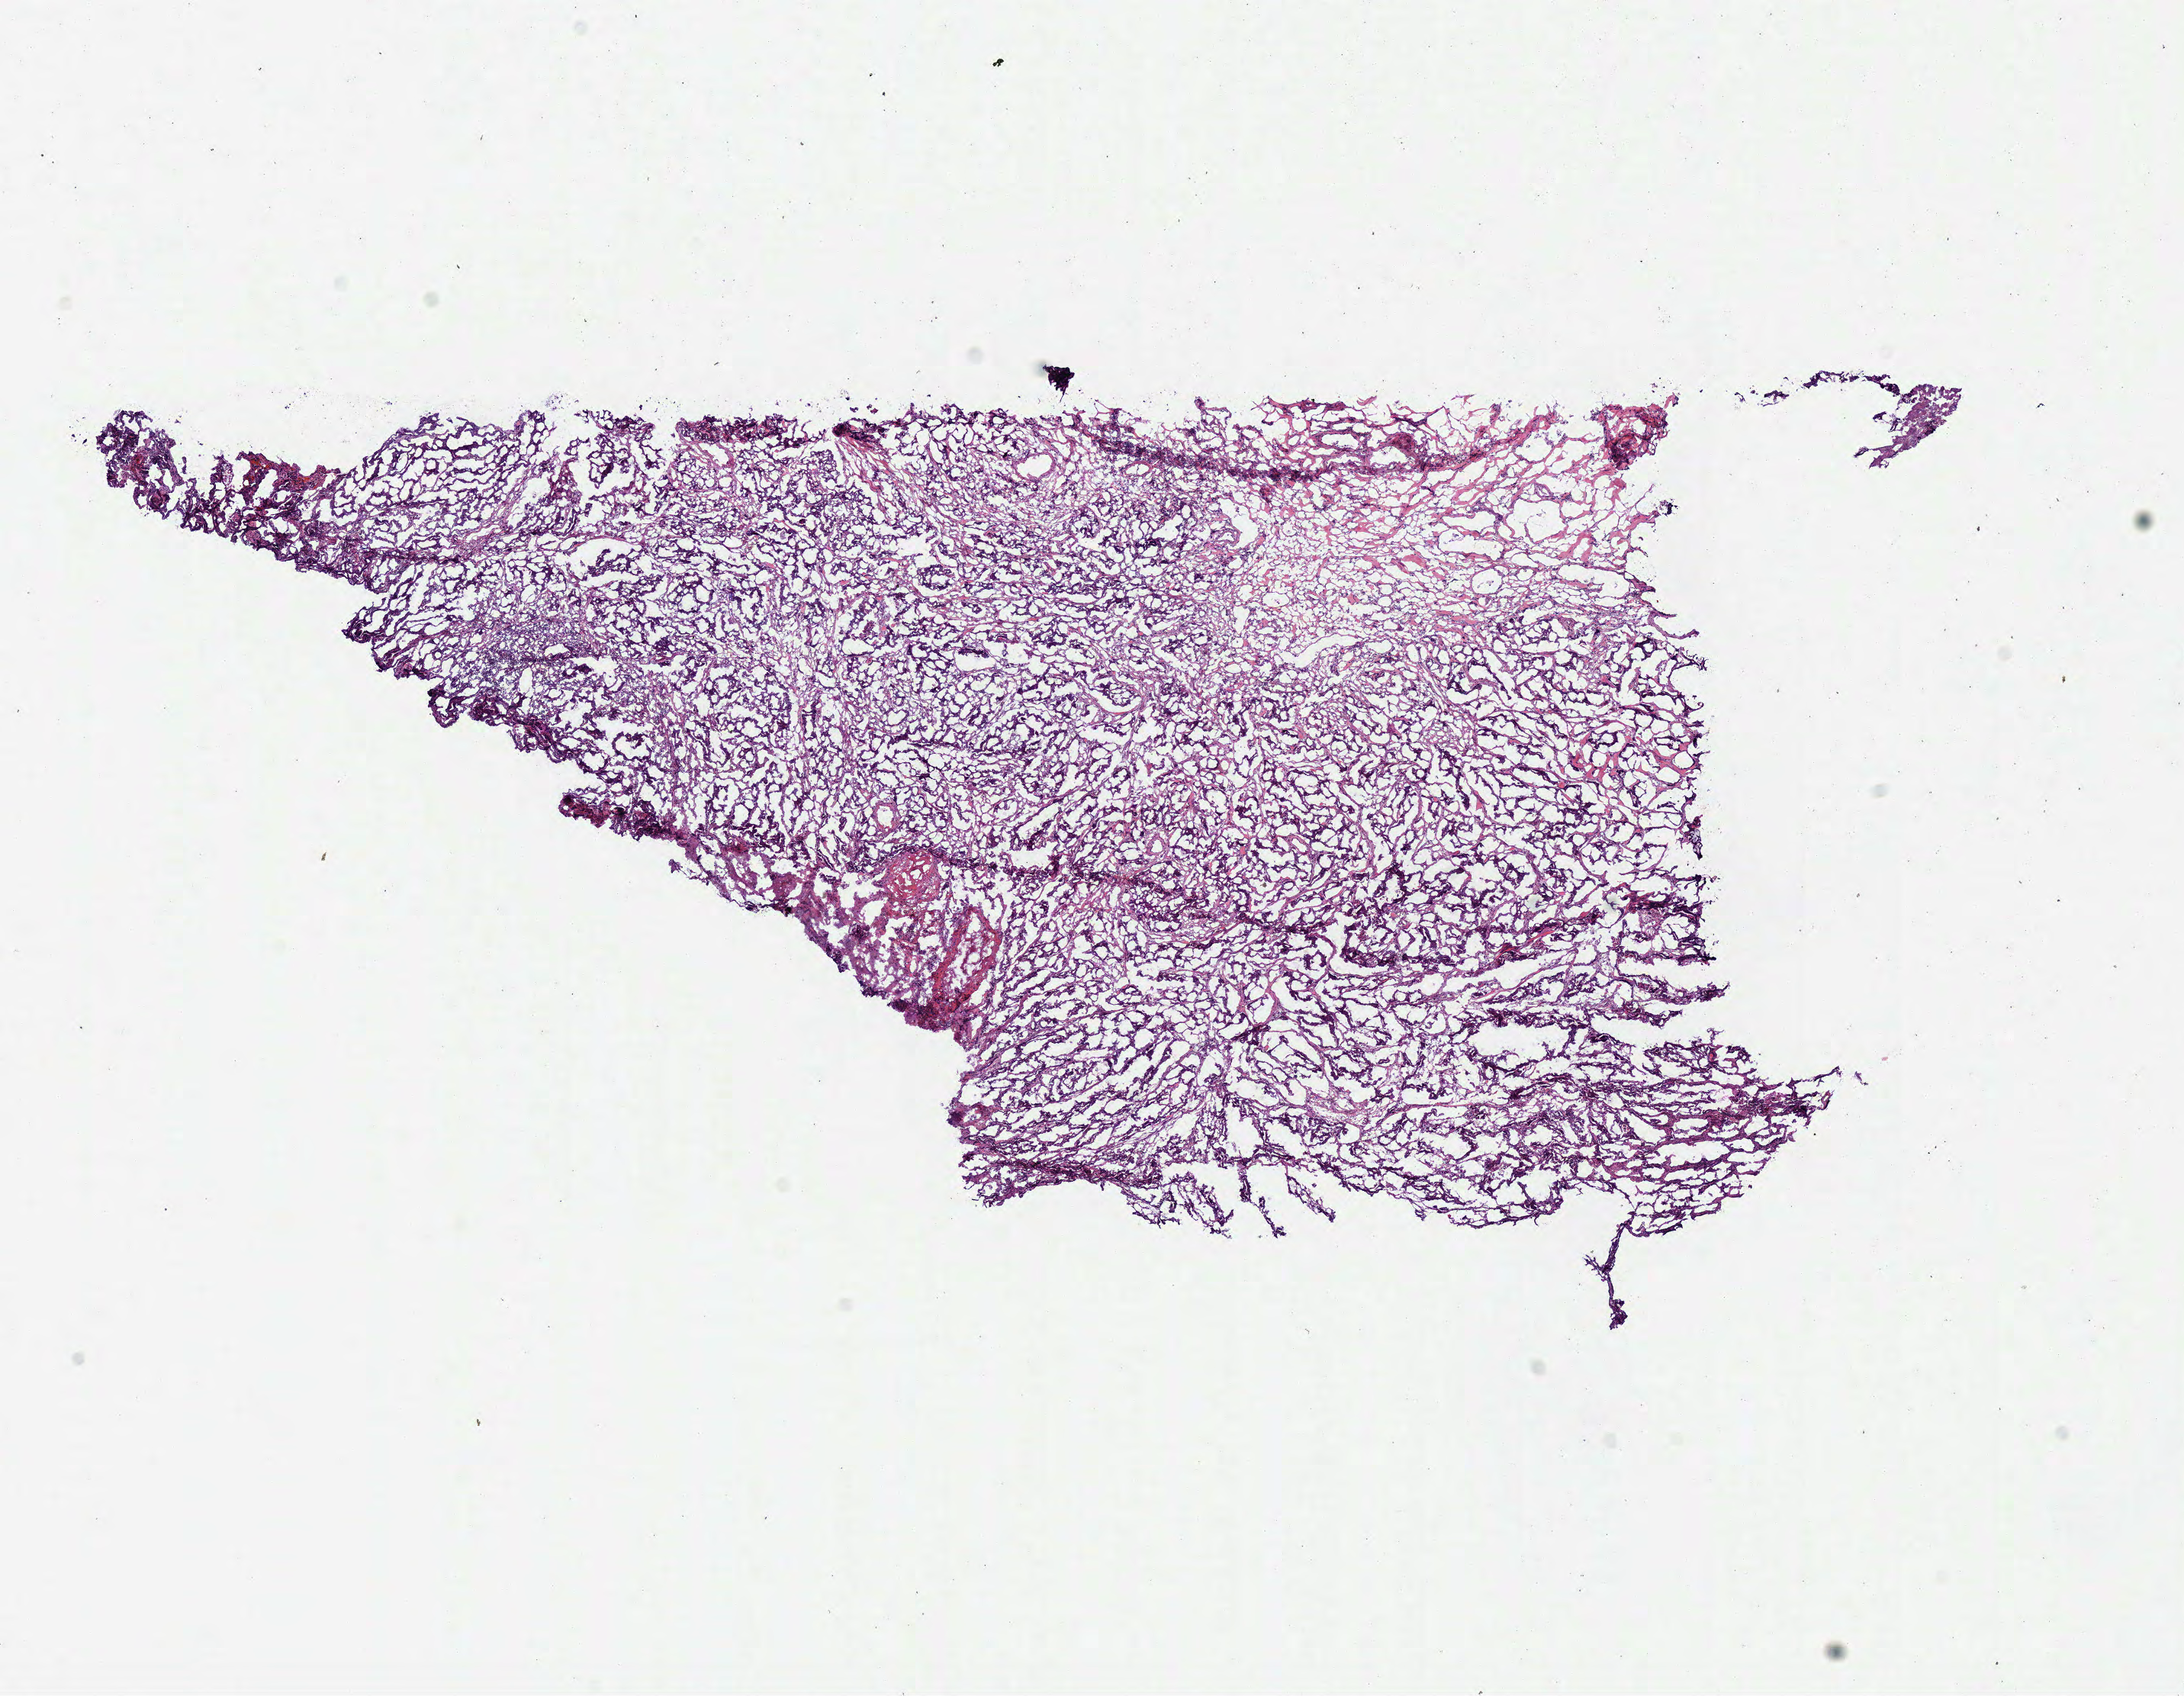
Whole-slide histology image, H&E-stained — low-resolution overview of the scanned area, about 11.3 x 8.7 mm, frozen section from the bottom of the tissue portion, primary tumour sample from the colon. Male patient. Composition of this section per pathologist review: tumour cells 75%, tumour nuclei 80%, normal cells 15%, stromal cells 10%, necrosis 0%.
• lymph nodes positive (case pathology): 1 of 37 examined
• diagnosis: Adenocarcinoma, NOS (cecum)
• AJCC pathologic stage: IIIB (6th edition)